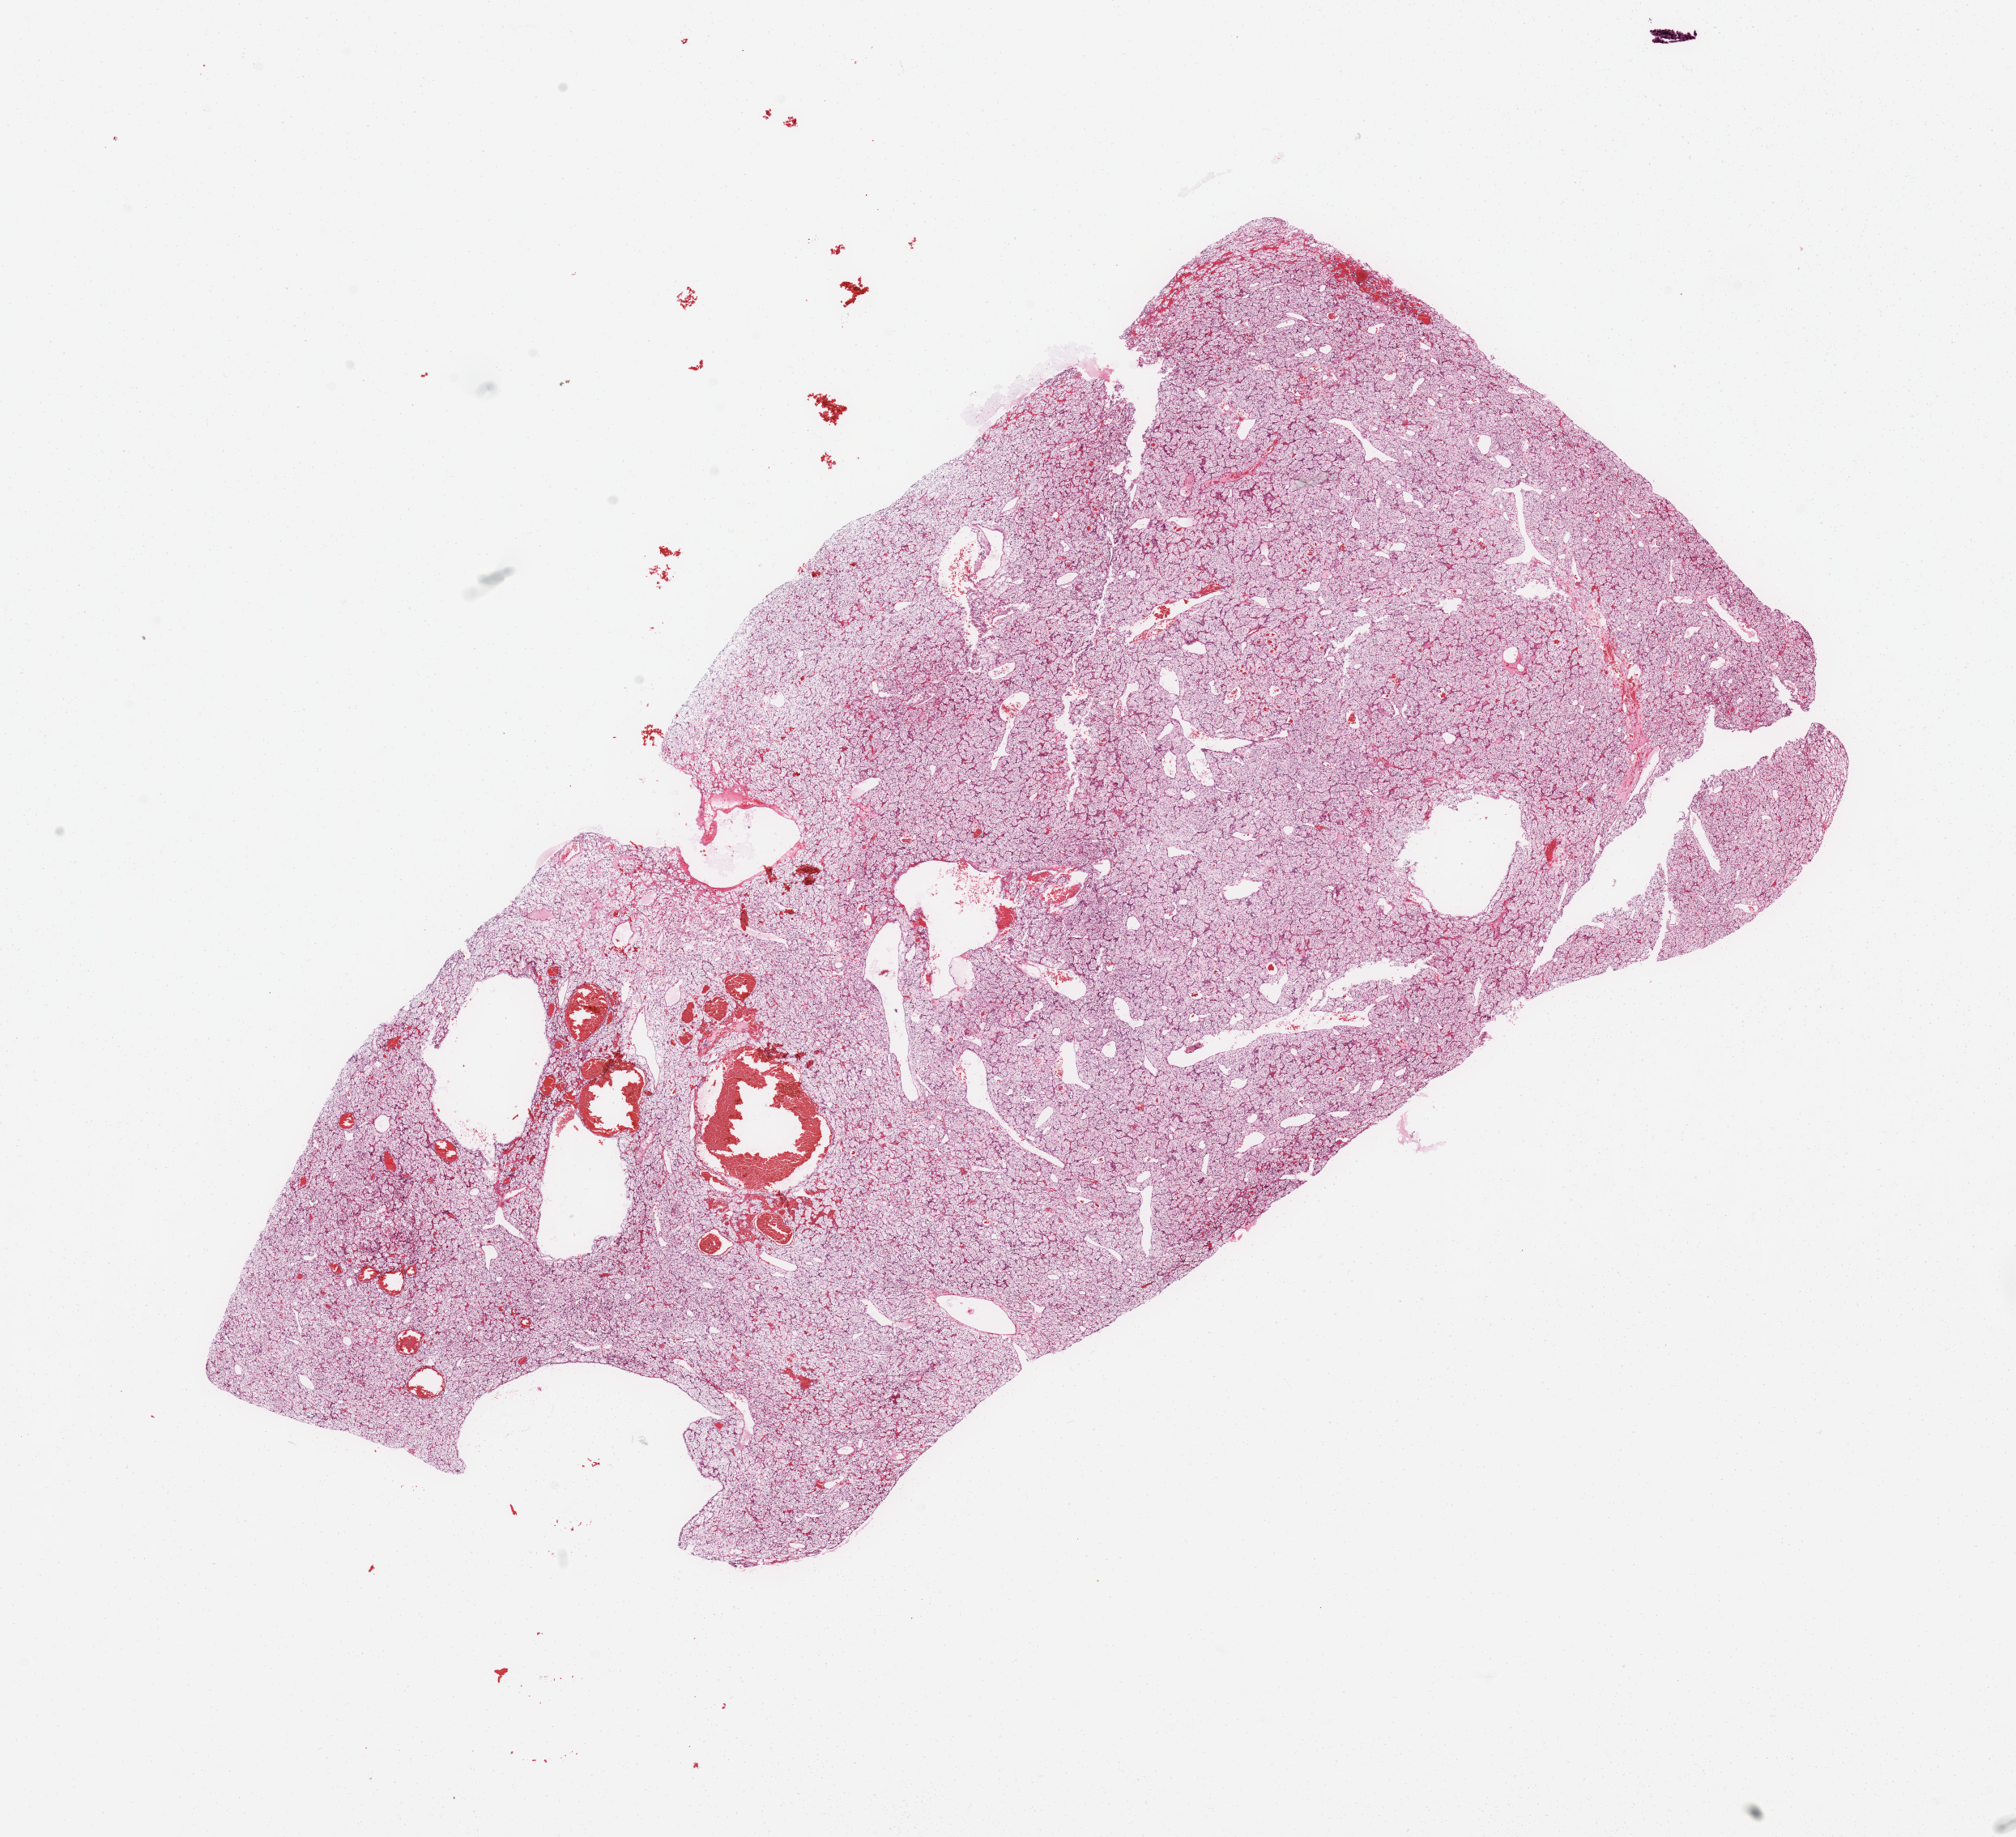
H&E whole-slide image — low-resolution overview of the scanned area, about 19.7 x 17.9 mm (from a 20x scan); tumour tissue sample, sampled site: kidney. Patient: female, age 56 years. Histologic grade: G2 (moderately differentiated). Pathologist review of this section (percent, as recorded): tumour nuclei 95%, necrosis 0%.
* diagnosis: Renal cell carcinoma, NOS
* AJCC pathologic stage: III